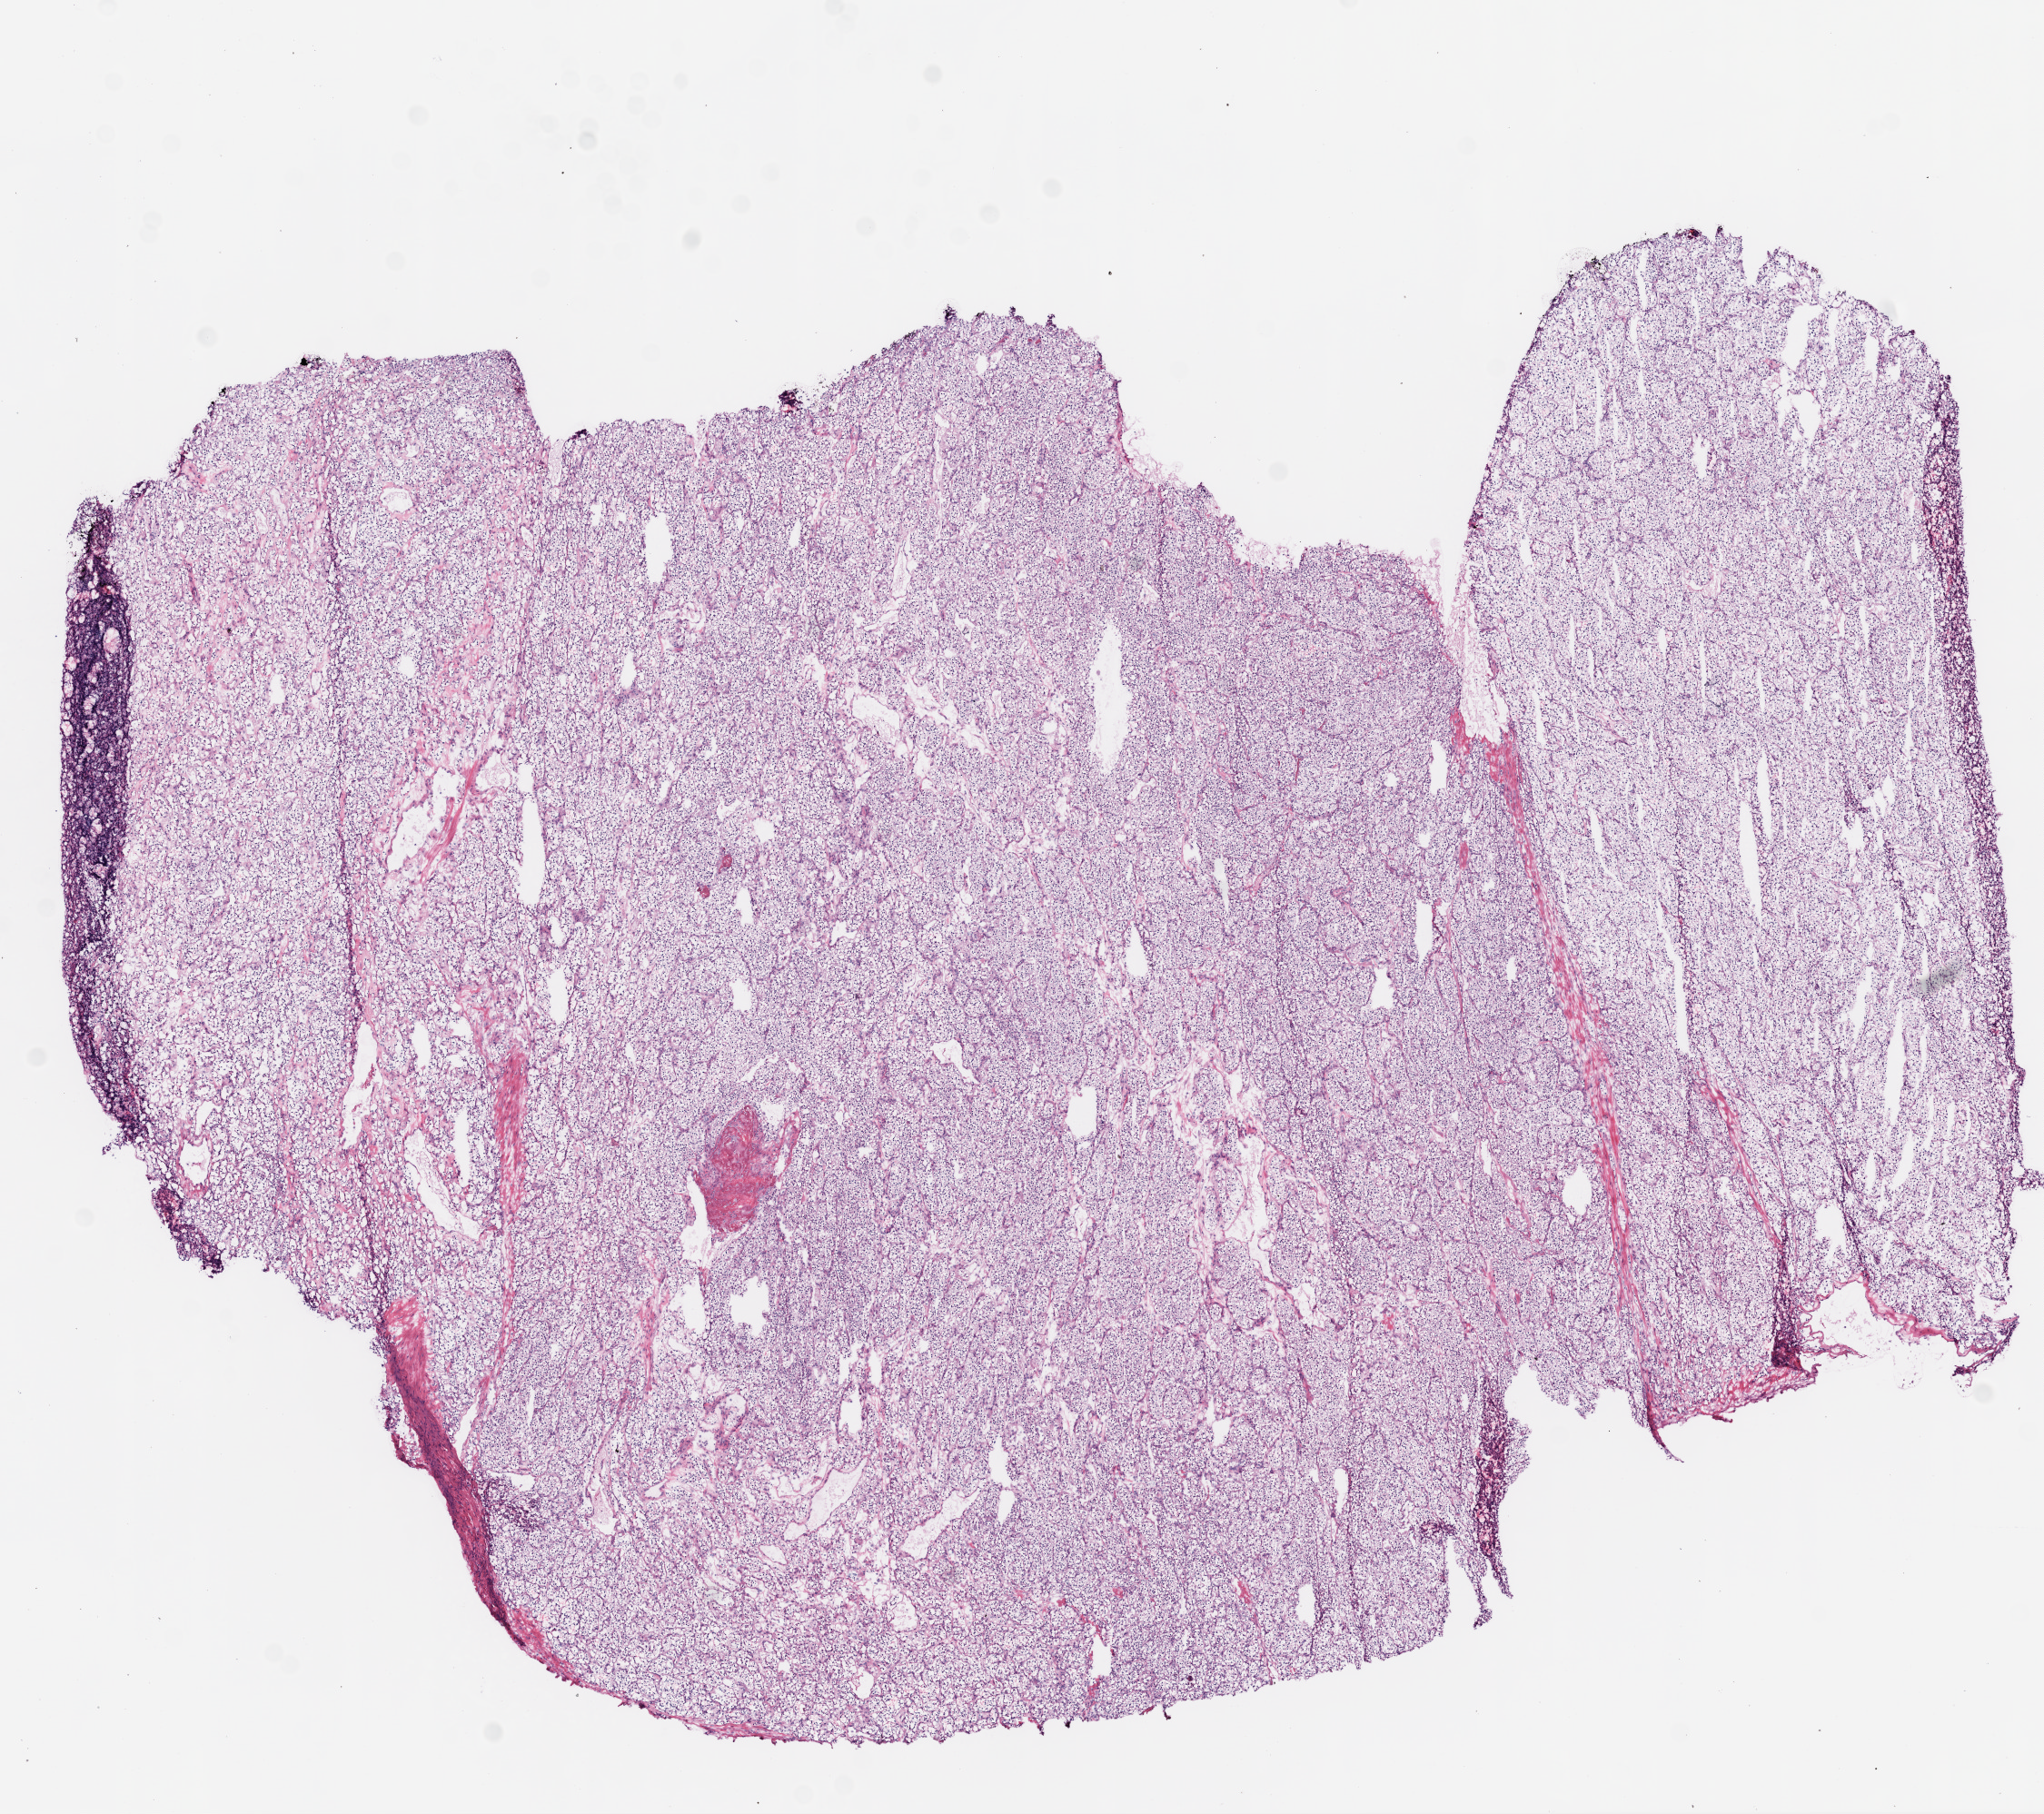
Whole-slide histology image, H&E — whole scanned area (about 9.0 x 8.0 mm, from a 20x scan) shown as a low-resolution overview; frozen section from the top of the tissue portion; primary tumour sample from the kidney. Female, age 52 years at initial diagnosis. Histologic grade: G1 (well differentiated). Pathologist review of this section (percent, as recorded): tumour cells 95%, tumour nuclei 90%, normal cells 0%, stromal cells 5%, necrosis 0%.
AJCC pathologic stage: I. Pathologic diagnosis: Clear cell adenocarcinoma, NOS.